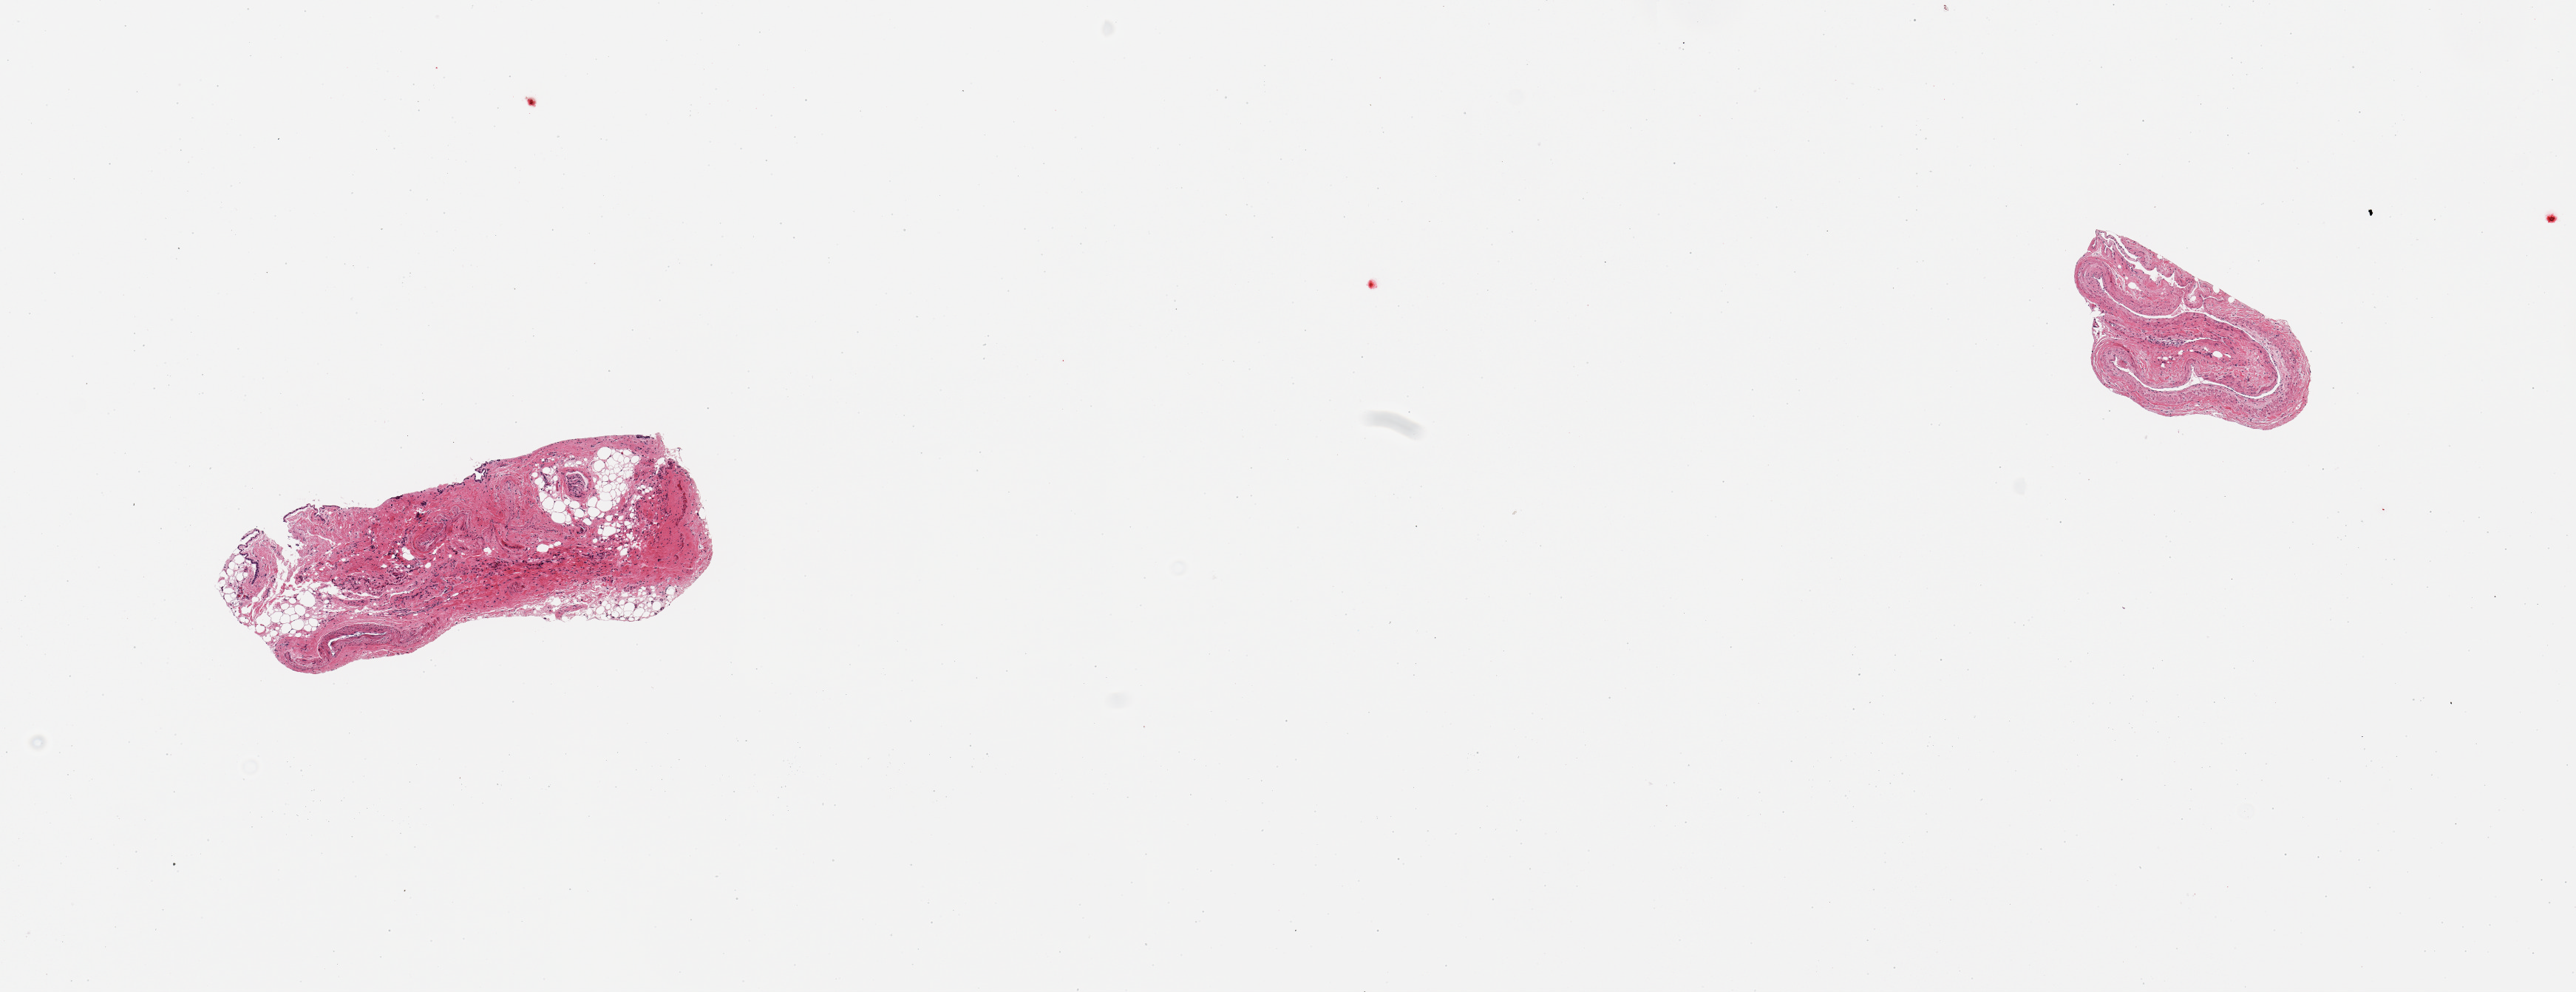
Digitized hematoxylin and eosin (H&E)-stained section — shown as a low-resolution overview of the whole scanned area (about 13.8 x 5.3 mm), PAXgene-fixed paraffin-embedded (PFPE) section, section of coronary artery (target tissue), tissue donor sample. Donor: female.
Reviewer comment on this tissue sample: 2 pieces fibroadipose/? sinus tissue, not coronary artery.